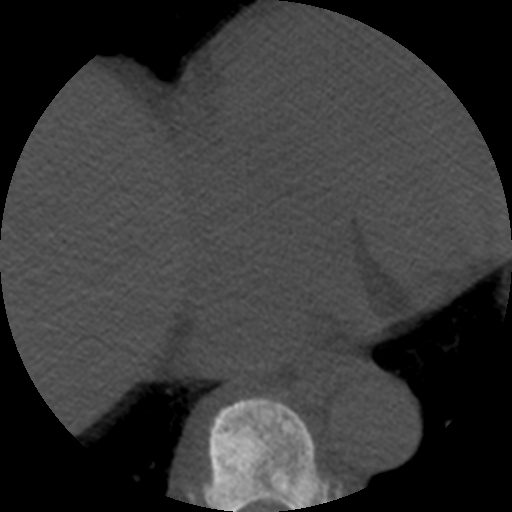
CT including the spine, one axial slice. Slice 308 of 508 in the series (ordered by position). Reconstruction kernel STANDARD. 120 kVp. Bone window (W 1800 / L 400 HU). 1.25 mm slice thickness. 512 × 512 image matrix, field of view 160 × 160 mm. Patient age 57 years. Case-level facts recorded for this patient, not image findings: primary cancer: prostate.
Structures marked on this image (semi-automatically segmented with operator editing):
- T8 vertebra: bounding box <203,397,330,512> (left, top, right, bottom; pixels)